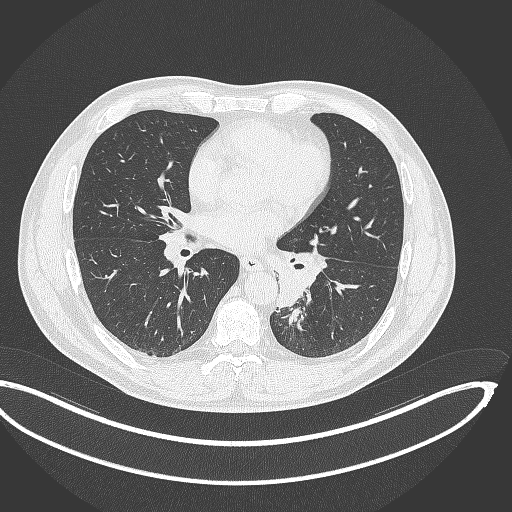
Chest CT, one axial slice; slice 168 of 362 in the series (ordered by position); lung window (W 1500 / L -600 HU); 512 × 512 image matrix, field of view 442 × 442 mm. Patient: male, 50 years. Case-level facts recorded for this patient, not image findings: clinical TNM (as recorded): T2a N3 M0.
Structures marked on this image (rectangle marked by the reading radiologist):
- lung tumour (recorded histology: squamous cell carcinoma): box from (x=267, y=249) to (x=329, y=312) px